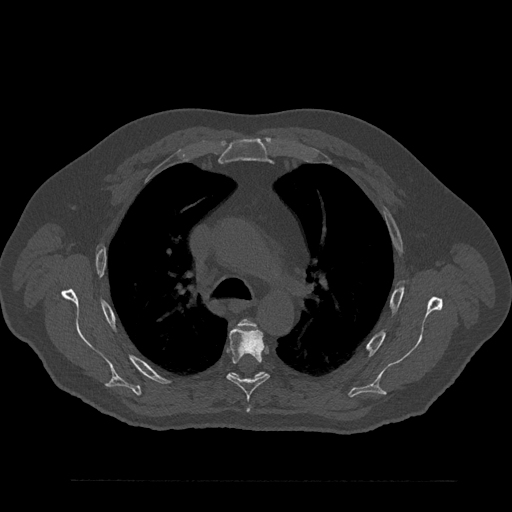
CT including the spine, one axial slice. Position 600 of 797 along the scan axis. Reconstruction kernel Br40s/3. Bone window (W 1800 / L 400 HU). 0.5 mm slice thickness. 512 × 512 image matrix, field of view 430 × 430 mm. Male patient, age 61 years. From the clinical record (not read from this slice): primary cancer: prostate.
Outlined on this slice (semi-automatically segmented with operator editing):
- T4 vertebra: box from (x=240, y=319) to (x=255, y=326) px
- T5 vertebra: (x=227, y=327)–(x=269, y=400)
- T6 vertebra: (x=229, y=372)–(x=266, y=381)